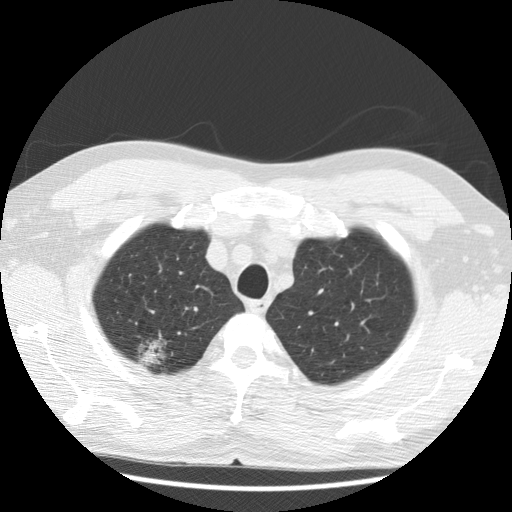
Axial slice from a low-dose chest CT screening exam. First (baseline) screen. Lung window (W 1500 / L -600 HU). 2.5 mm slice thickness. Standard (soft-tissue) reconstruction kernel (STANDARD). 120 kVp. 512 × 512 image matrix, field of view 350 × 350 mm. Male, age 59 years at enrolment. Former smoker at enrolment.
Expert reader's lesion annotation, bounding box <126,329,181,382> (left, top, right, bottom; pixels). Reader record for this screening exam (exam-level; its link to the box is not recorded): non-calcified nodule or mass ≥4 mm, right upper lobe, 30 × 28 mm, poorly defined margins, ground glass attenuation. Official screen result: positive, change unspecified: nodule(s) >= 4 mm or enlarging nodule(s), mass(es), or other non-specific abnormalities suspicious for lung cancer. Participant outcome: lung cancer diagnosed 40 days after this screen — bronchiolo-alveolar carcinoma, non-mucinous, right upper lobe, well differentiated (G1), stage IA (AJCC 6th edition), 15 mm at pathology.